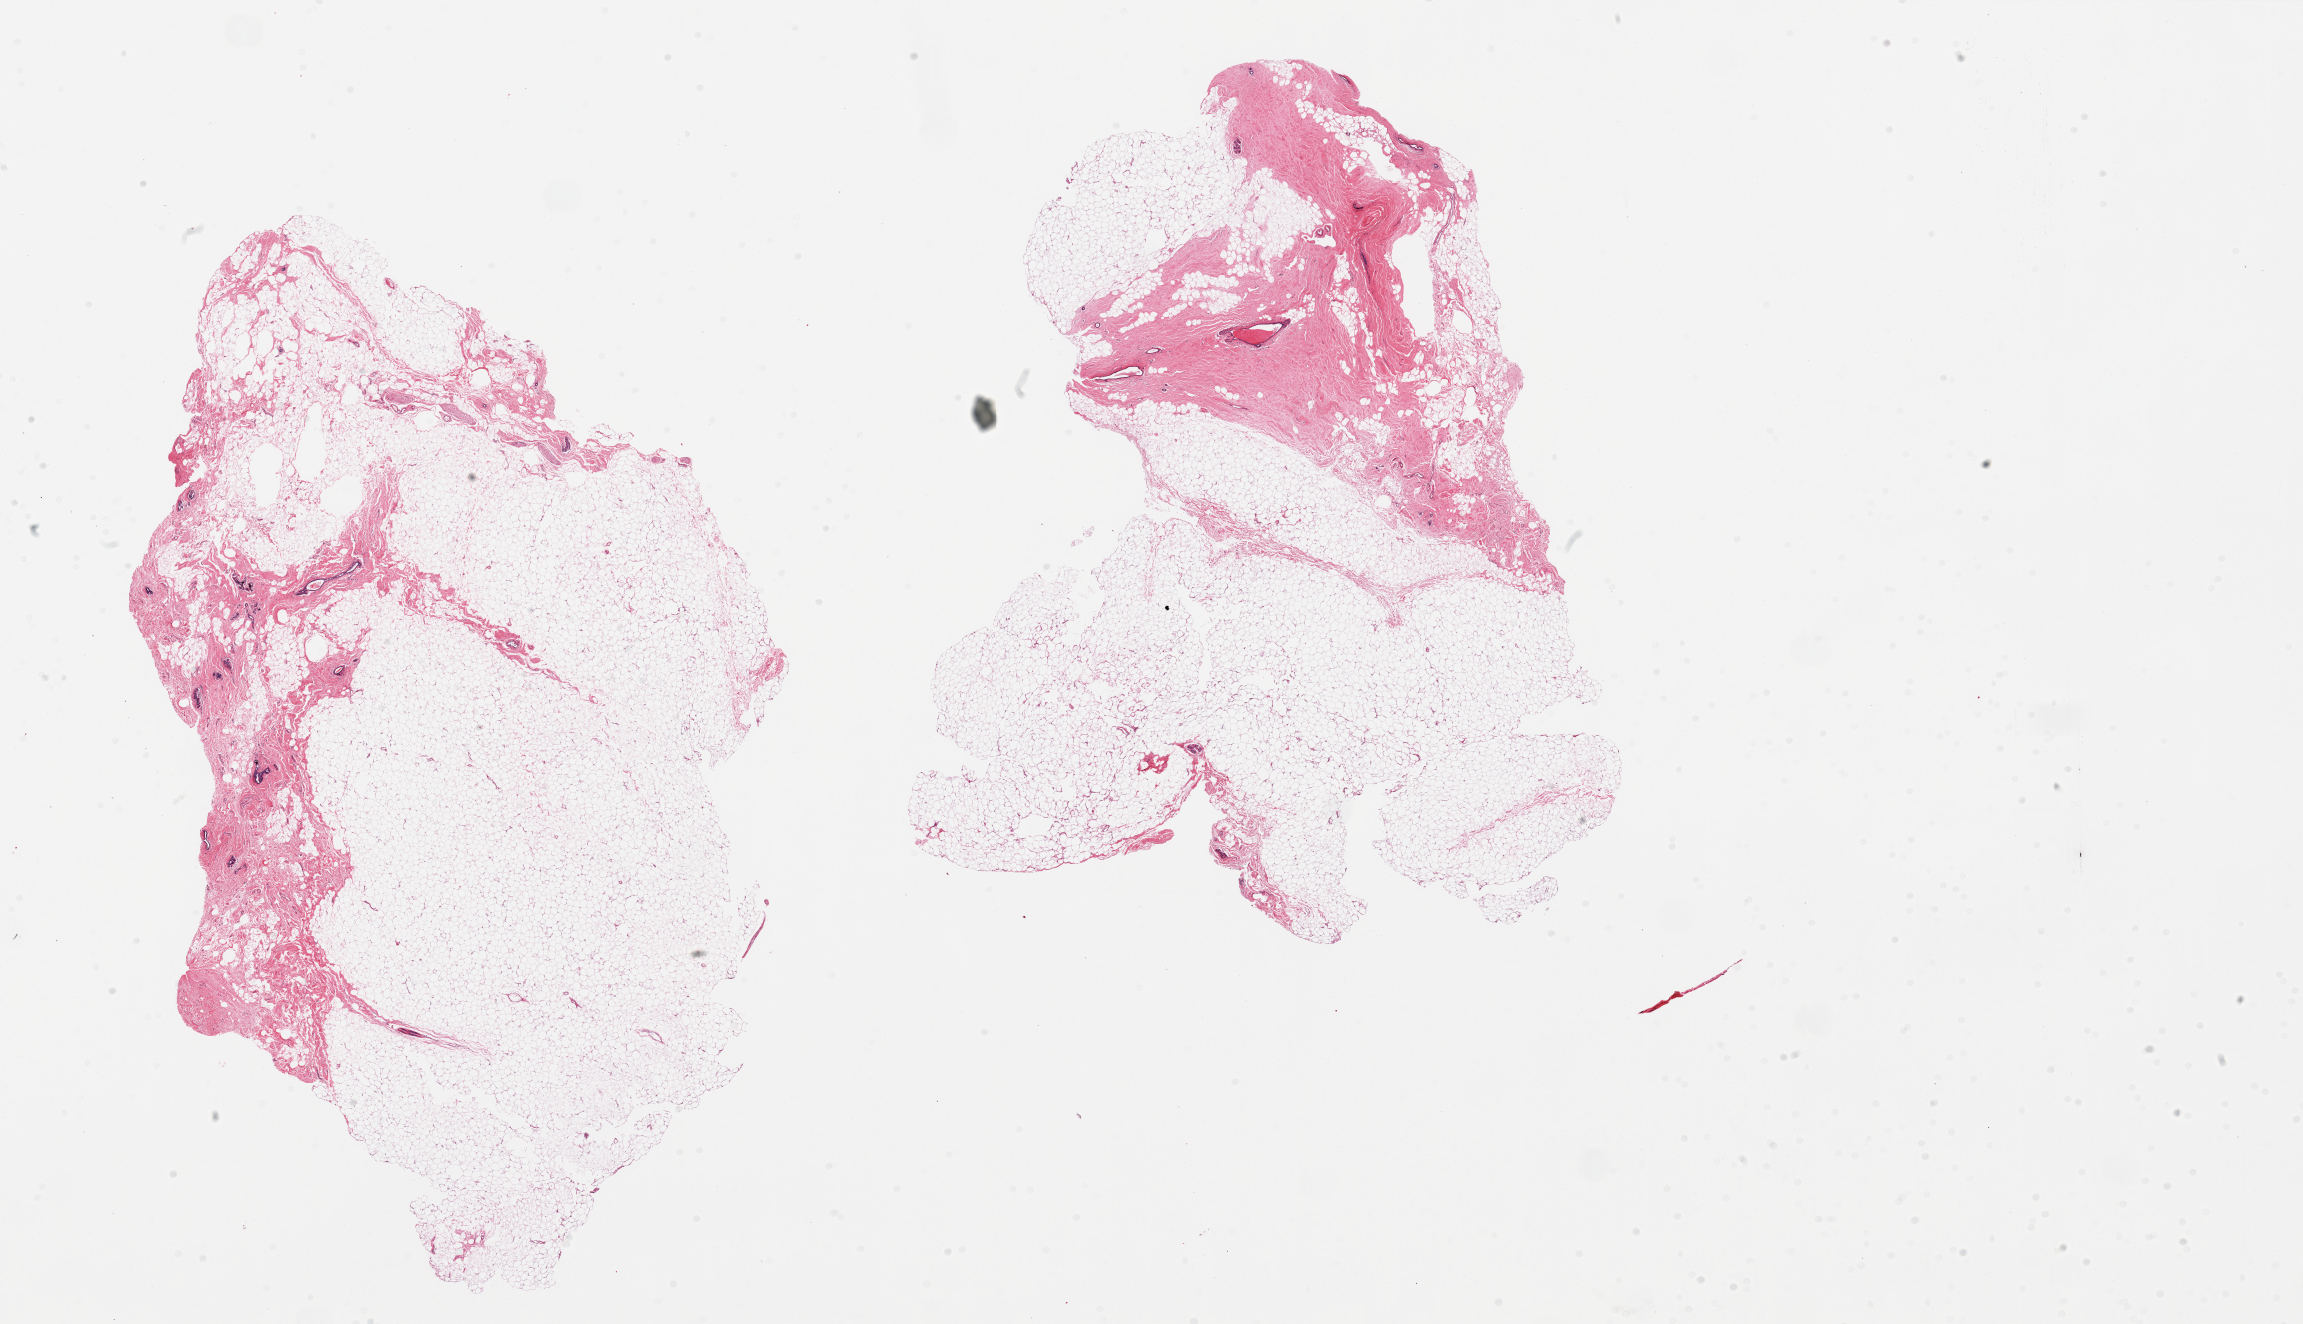
H&E whole-slide image — a low-resolution overview of the entire scanned area, about 36.4 x 20.9 mm (from a 20x scan), PAXgene-fixed, paraffin-embedded tissue, target tissue: breast, tissue donor sample. Donor: female.
Reviewer comment on this tissue sample: 2 pieces, predominantly fatty with 10-20% fibrous stroma and ductal/lobular elements, microcalciifcations.